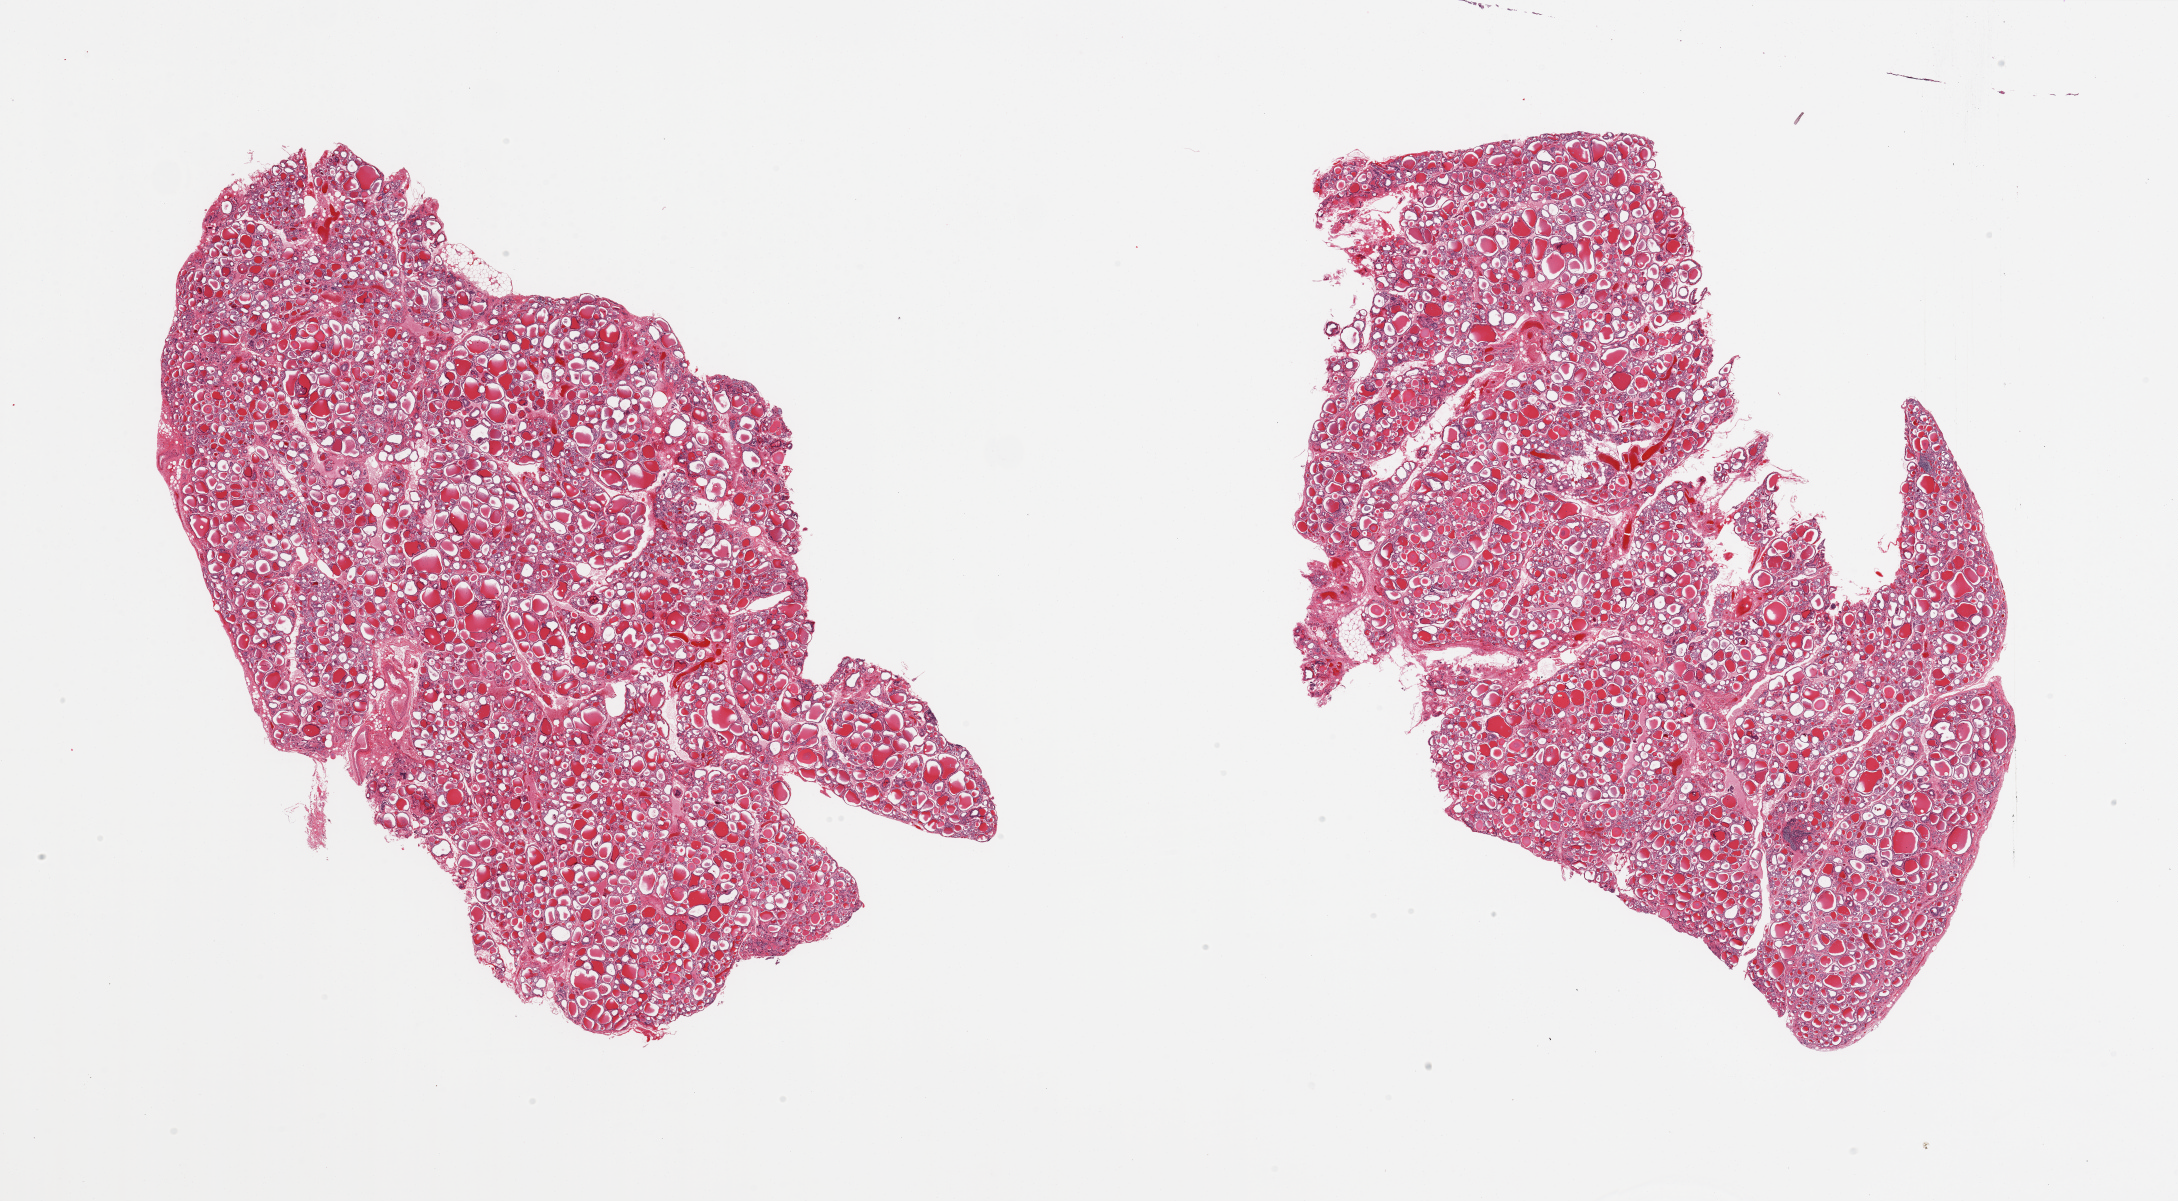
Digitized H&E-stained section, whole scanned area (about 34.5 x 19.0 mm) shown as a low-resolution overview, PAXgene-fixed, paraffin-embedded tissue, target tissue: thyroid, donor tissue sample. Male donor.
Review note (as recorded): 2 pieces; mild lymphocytic infiltrate.